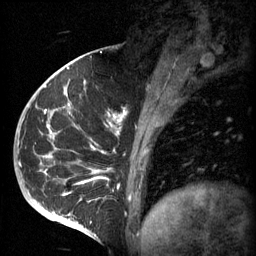
Breast MRI (dynamic contrast-enhanced), one sagittal slice; position 24 of 60 along the scan axis; 3 images stored at this slice position (order not interpretable as contrast timing); 1.5 T; TE 4.2 ms, TR 11 ms; 2 mm slice thickness; 256 × 256 image matrix. Patient: female, 51 years.
Outlined on this slice (semi-automatically segmented with operator editing):
- analysis volume of interest (the breast-tissue region the enhancement analysis was run in; not a lesion): box from (x=48, y=82) to (x=161, y=197) px
- tumour enhancement mask (voxels above the 70 % enhancement threshold inside the analysis volume of interest): (x=48, y=82)–(x=147, y=195)